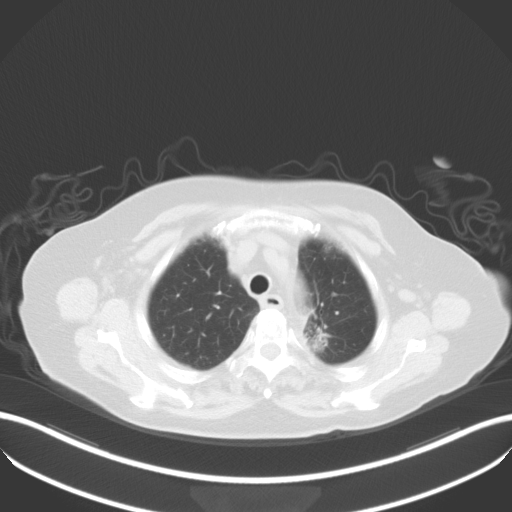
Chest CT, one axial slice; position 33 of 42 along the scan axis; reconstruction kernel B31f; lung window (W 1500 / L -600 HU); 6 mm slice thickness; 512 × 512 image matrix, field of view 400 × 400 mm. Female patient, age 81 years. Case-level facts recorded for this patient, not image findings: clinical TNM (as recorded): T2a N0 M0.
Annotated regions visible in this slice (bounding box drawn by a radiologist):
- lung tumour (recorded histology: adenocarcinoma): box from (x=284, y=315) to (x=331, y=361) px